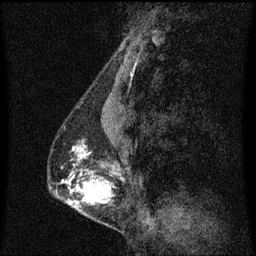
Breast MRI (dynamic contrast-enhanced), one sagittal slice. Position 24 of 60 along the scan axis. Dynamic contrast-enhanced series, image 2 of 3 at this slice position (ordered by acquisition). 1.5 T. TE 4.2 ms, TR 8.4 ms. 256 × 256 image matrix, field of view 200 × 200 mm. Female patient, age 40 years. Case-level facts recorded for this patient, not image findings: setting: breast cancer imaged before/during neoadjuvant chemotherapy; receptor status: triple-negative.
Outlined on this slice (semi-automatically segmented with operator editing):
- analysis volume of interest (the breast-tissue region the enhancement analysis was run in; not a lesion): bounding box <57,128,120,211> (left, top, right, bottom; pixels)
- tumour enhancement mask (voxels above the 70 % enhancement threshold inside the analysis volume of interest): <80,150,111,203>